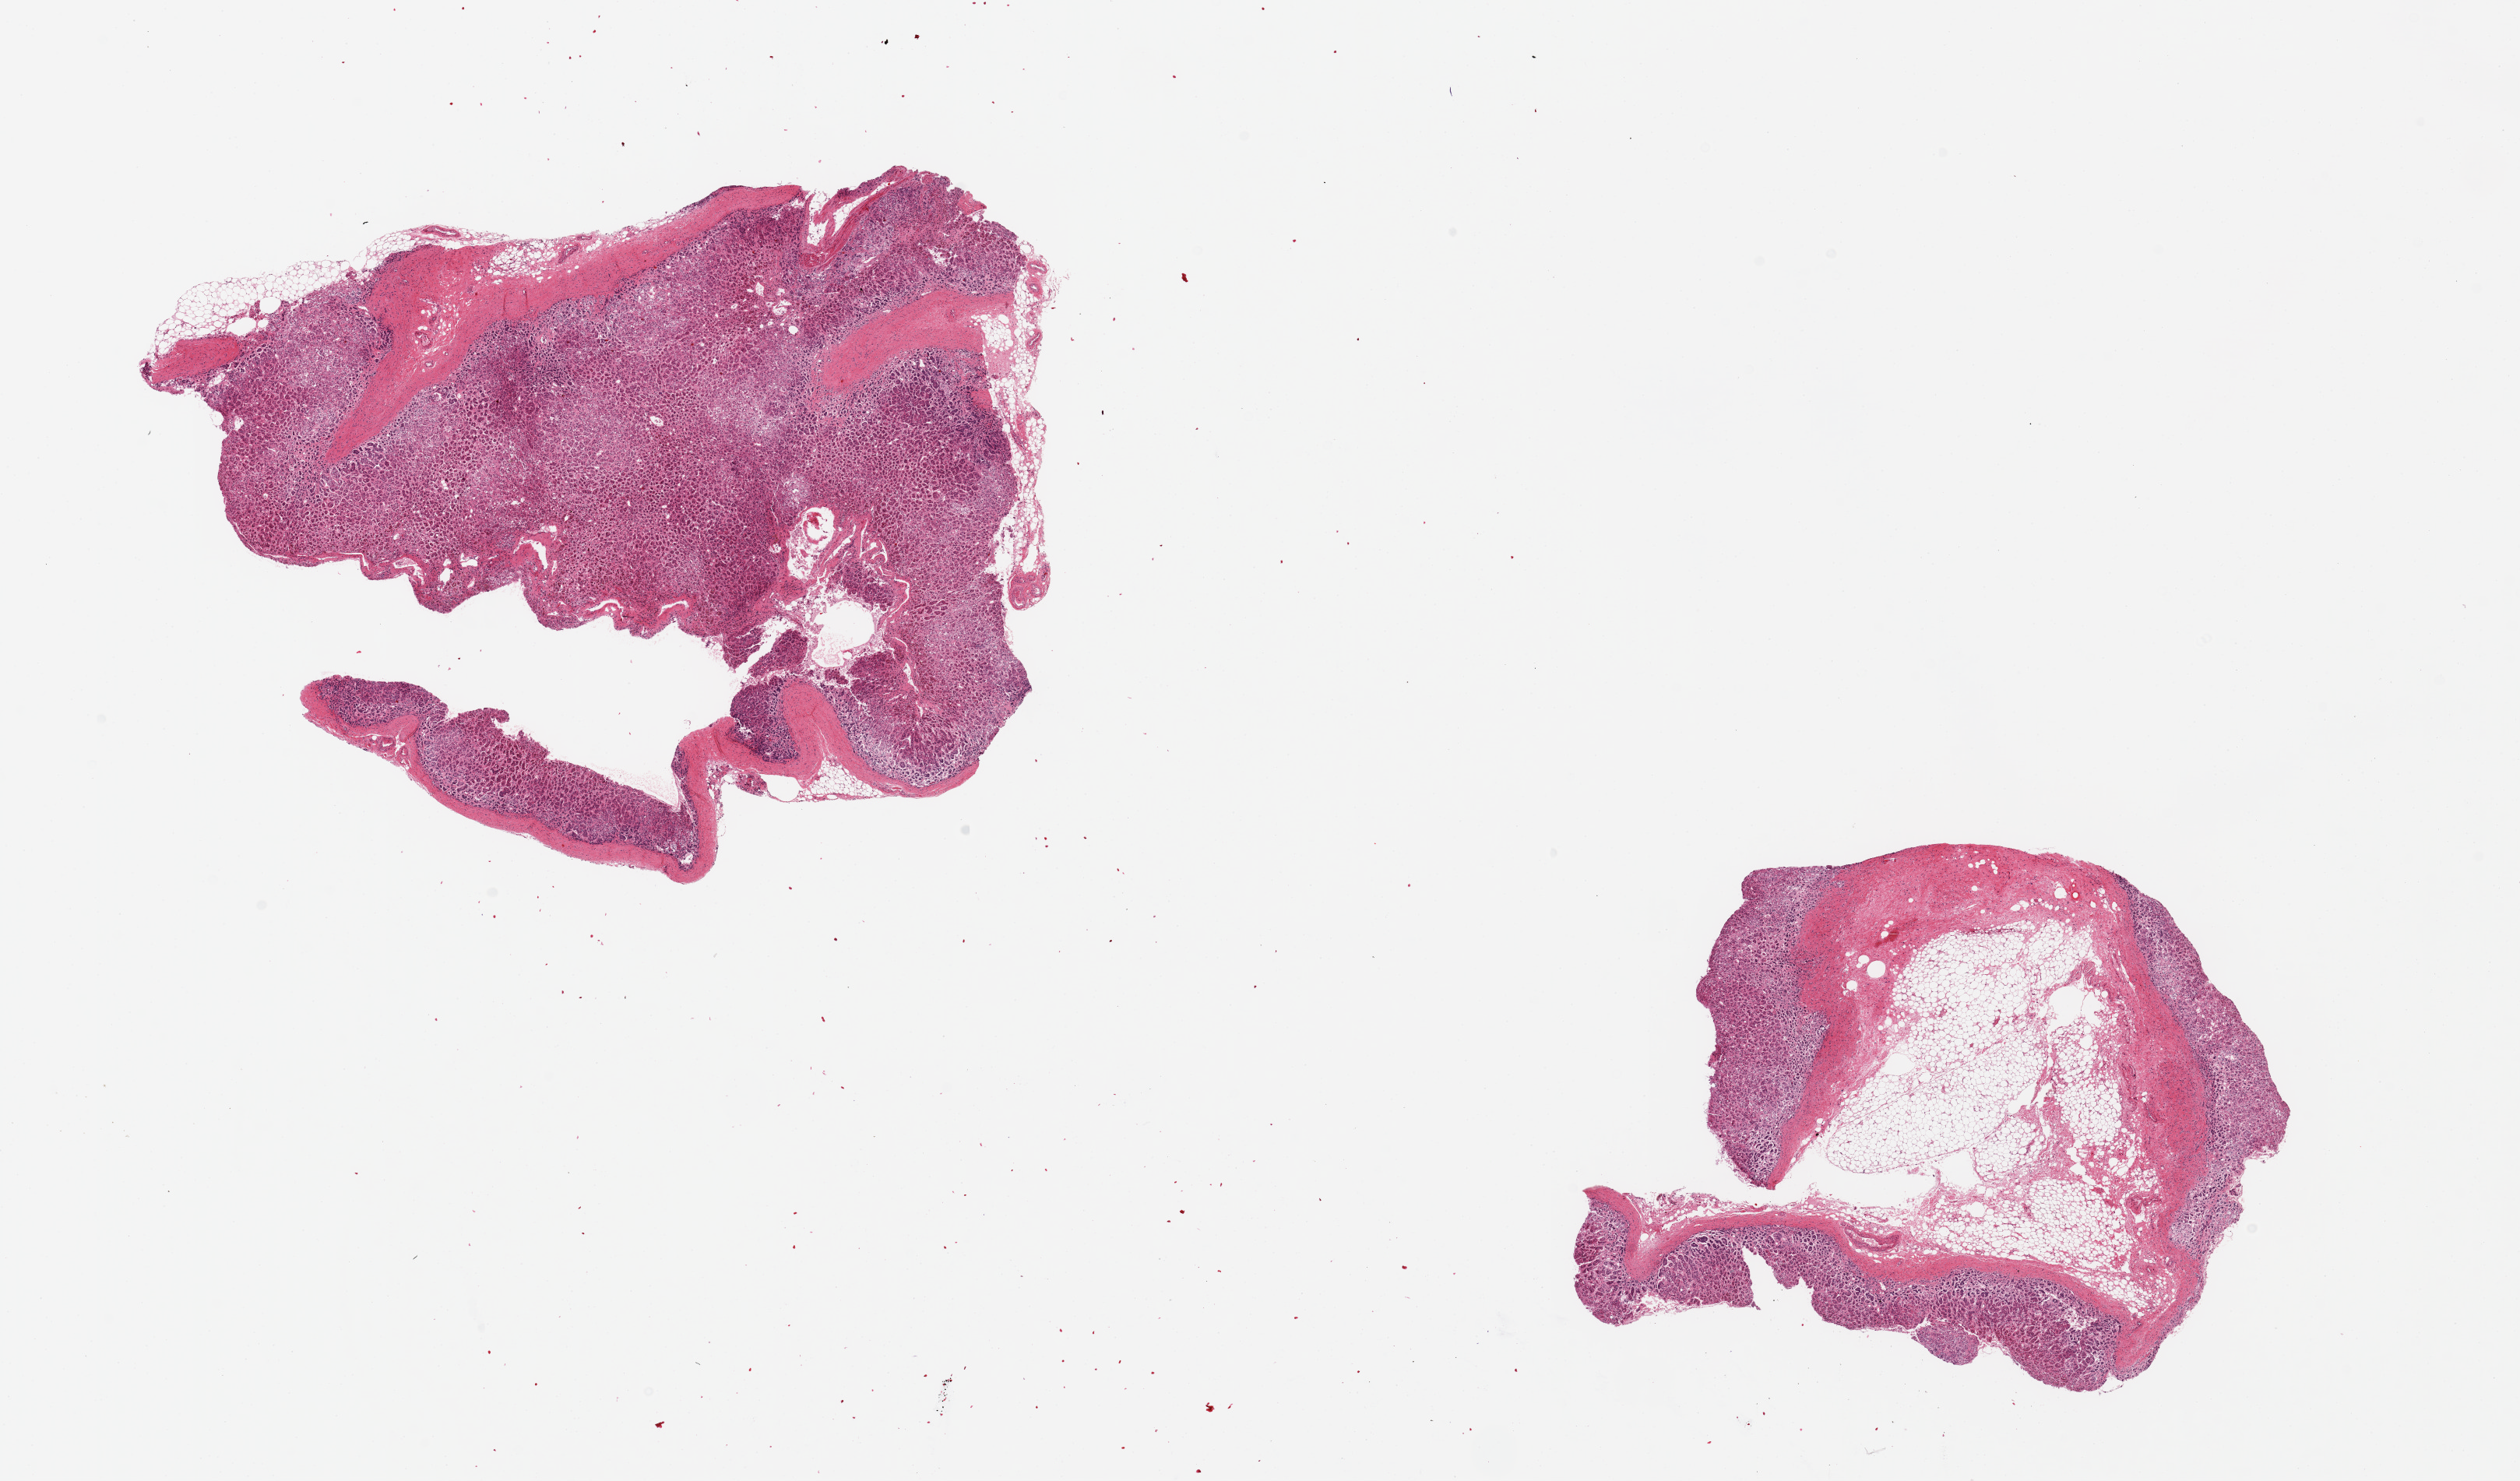
Hematoxylin and eosin (H&E) whole-slide image — shown as a low-resolution overview of the whole scanned area (about 25.6 x 15.0 mm). PAXgene-fixed paraffin-embedded (PFPE) section. Target tissue: adrenal gland. Tissue donor sample.
- pathologist's review note for this sample: 2 pieces, 8x7 & 6x5.5mm; the smaller piece contains 80% adipose